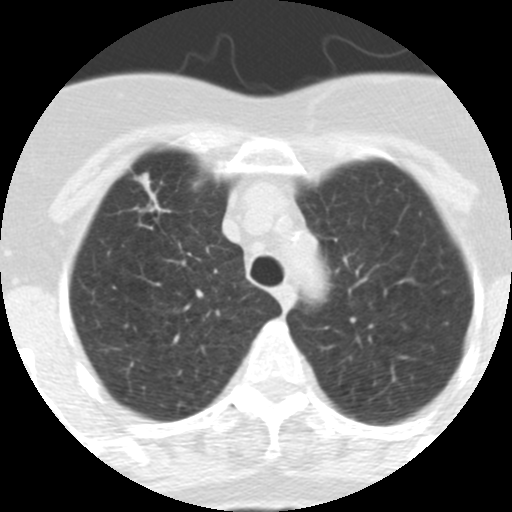
Low-dose screening chest CT, axial slice; first (baseline) screen; lung window (W 1500 / L -600 HU); 2.5 mm slice thickness; slice 64 of 313 in the series; 512 × 512 image matrix, field of view 253 × 253 mm. Female participant, aged 62 years at enrolment.
- Expert-annotated lung lesion, bounding box [x1, y1, x2, y2] px = [116, 168, 188, 236].
- Reader record for this screening exam (exam-level; its link to the box is not recorded): non-calcified nodule or mass ≥4 mm, right upper lobe, 9 × 7 mm, spiculated (stellate) margins, soft tissue attenuation.
- Later outcome: lung cancer diagnosed 126 days after this screen — adenocarcinoma, NOS, right upper lobe, moderately differentiated (G2), stage IA (AJCC 6th edition), 18 mm at pathology.